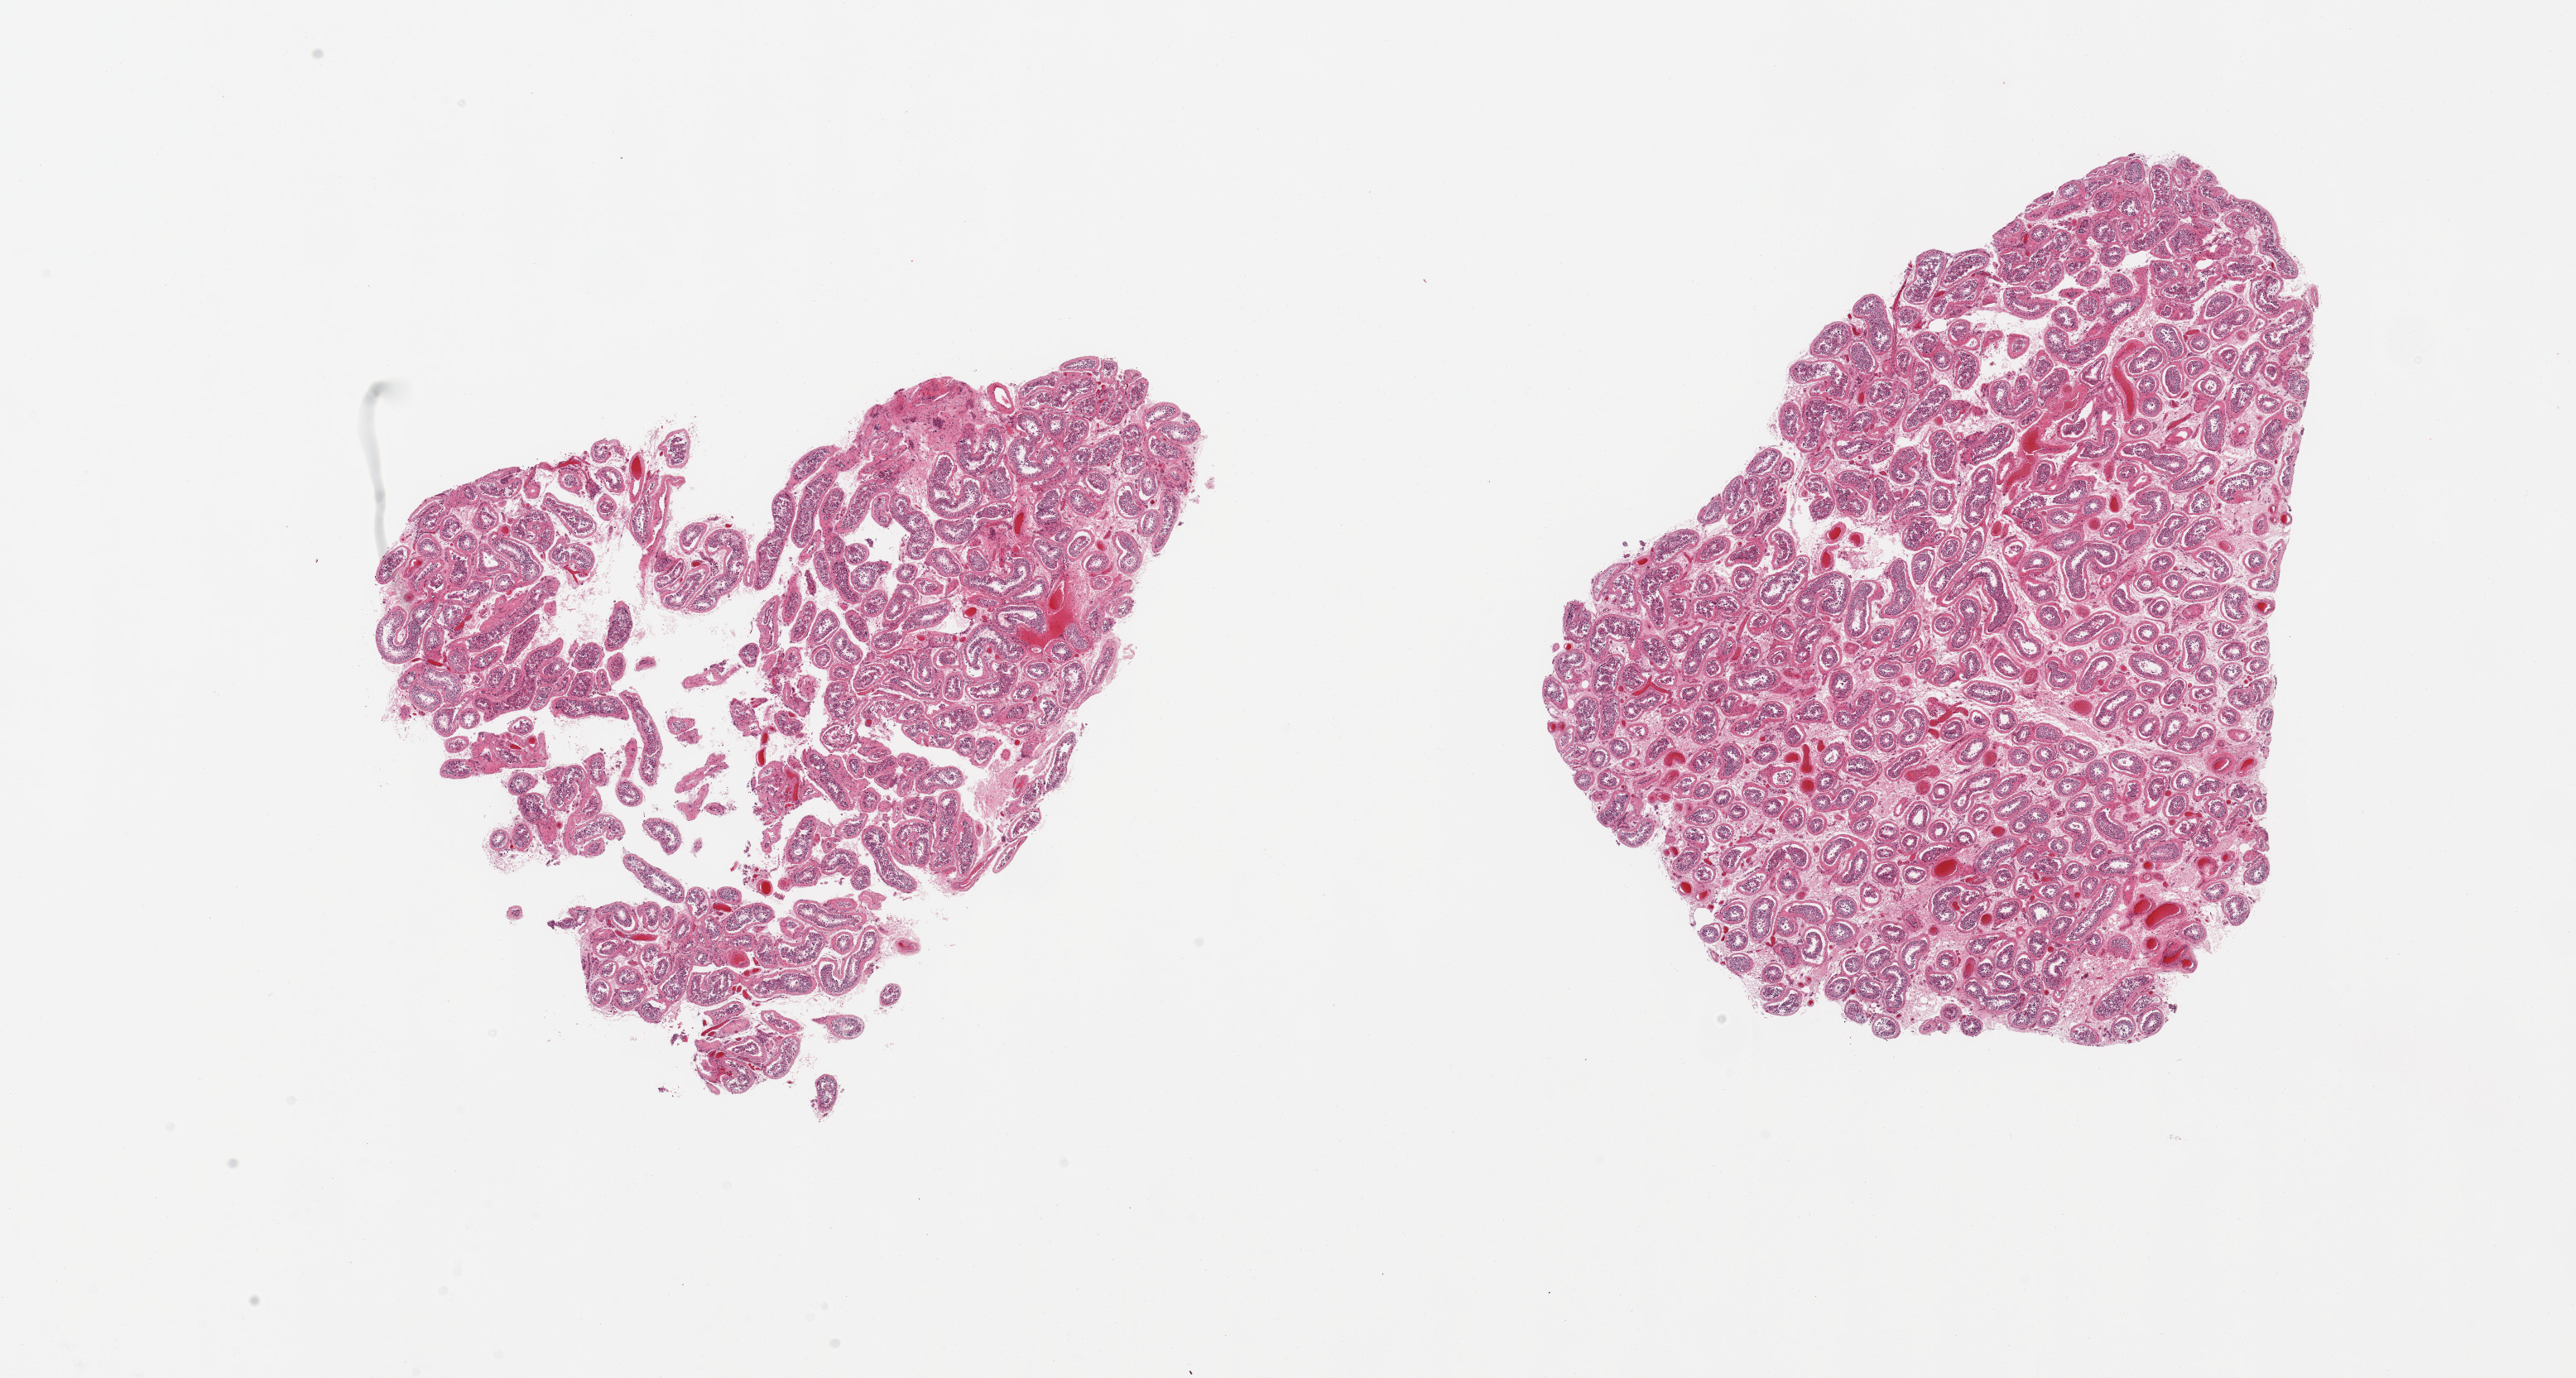
Digitized H&E-stained section, a low-resolution overview of the entire scanned area, about 24.6 x 13.2 mm, PAXgene-fixed, paraffin-embedded tissue, section of testis (target tissue), tissue donor sample.
Review note (as recorded): 2 pieces; congestion; decreased spermatogenesis.